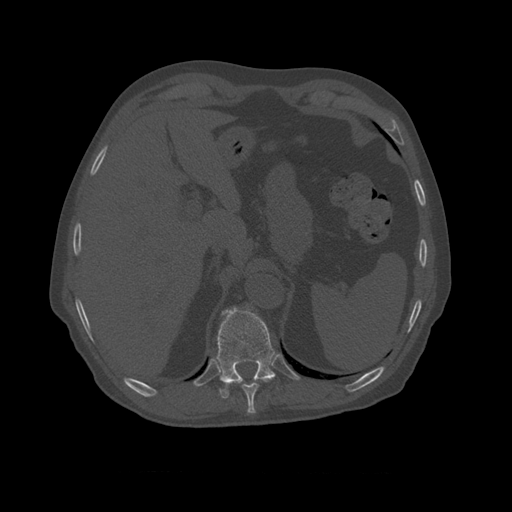
CT including the spine, one axial slice. Position 409 of 450 along the scan axis. Bone window (W 1800 / L 400 HU). 1.25 mm slice thickness. 512 × 512 image matrix. Patient age 75 years. From the clinical record (not read from this slice): primary cancer: prostate.
Outlined on this slice (semi-automatically segmented with operator editing):
- T10 vertebra: bounding box <216,307,279,399> (left, top, right, bottom; pixels)
- T9 vertebra: <242,380,268,410>